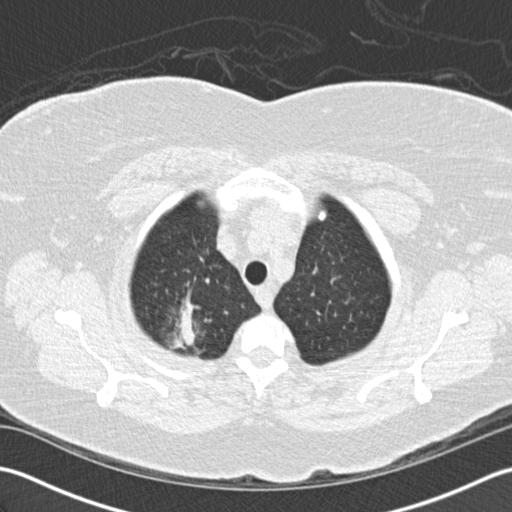
Axial slice from a low-dose chest CT screening exam. Baseline screening round. Lung window (W 1500 / L -600 HU). 2 mm slice thickness. 120 kVp. Female participant, aged 72 years at enrolment.
- Expert-annotated lung lesion, bounding box (x1, y1, x2, y2) in pixels: (136, 276, 227, 367).
- The screening reader recorded 2 non-calcified nodules or masses ≥4 mm on this exam; which of them this box marks is not recorded.
- Official screen result: positive, change unspecified: nodule(s) >= 4 mm or enlarging nodule(s), mass(es), or other non-specific abnormalities suspicious for lung cancer.
- Later outcome: lung cancer diagnosed 494 days after this screen (after the second annual screen) — bronchiolo-alveolar adenocarcinoma, NOS, right upper lobe, stage IIIB (AJCC 6th edition), 45 mm at pathology.